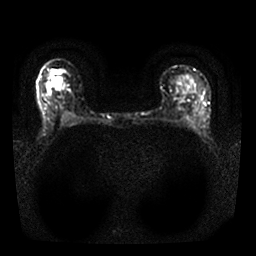
Breast MRI, one axial slice; position 16 of 25 along the scan axis; diffusion-weighted series; image 2 of 4 stored at this slice position (different b-values; order by instance number); 1.5 T; 256 × 256 image matrix. Female patient.
Annotated regions visible in this slice (manually delineated by an expert):
- tumour on diffusion-weighted imaging: box from (x=52, y=77) to (x=60, y=82) px